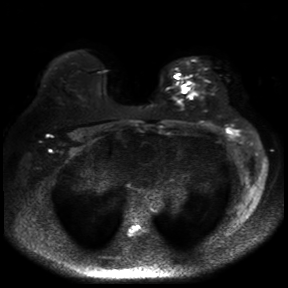
Breast MRI, one axial slice. Slice 24 of 30 in the series (ordered by position). Diffusion-weighted series; image 2 of 4 stored at this slice position (different b-values; order by instance number). 3 T. 4 mm slice thickness. 288 × 288 image matrix, field of view 360 × 360 mm. Female patient.
Annotated regions visible in this slice (outlined manually by an expert reader):
- tumour on diffusion-weighted imaging: bounding box [x1, y1, x2, y2] px = [180, 88, 192, 99]